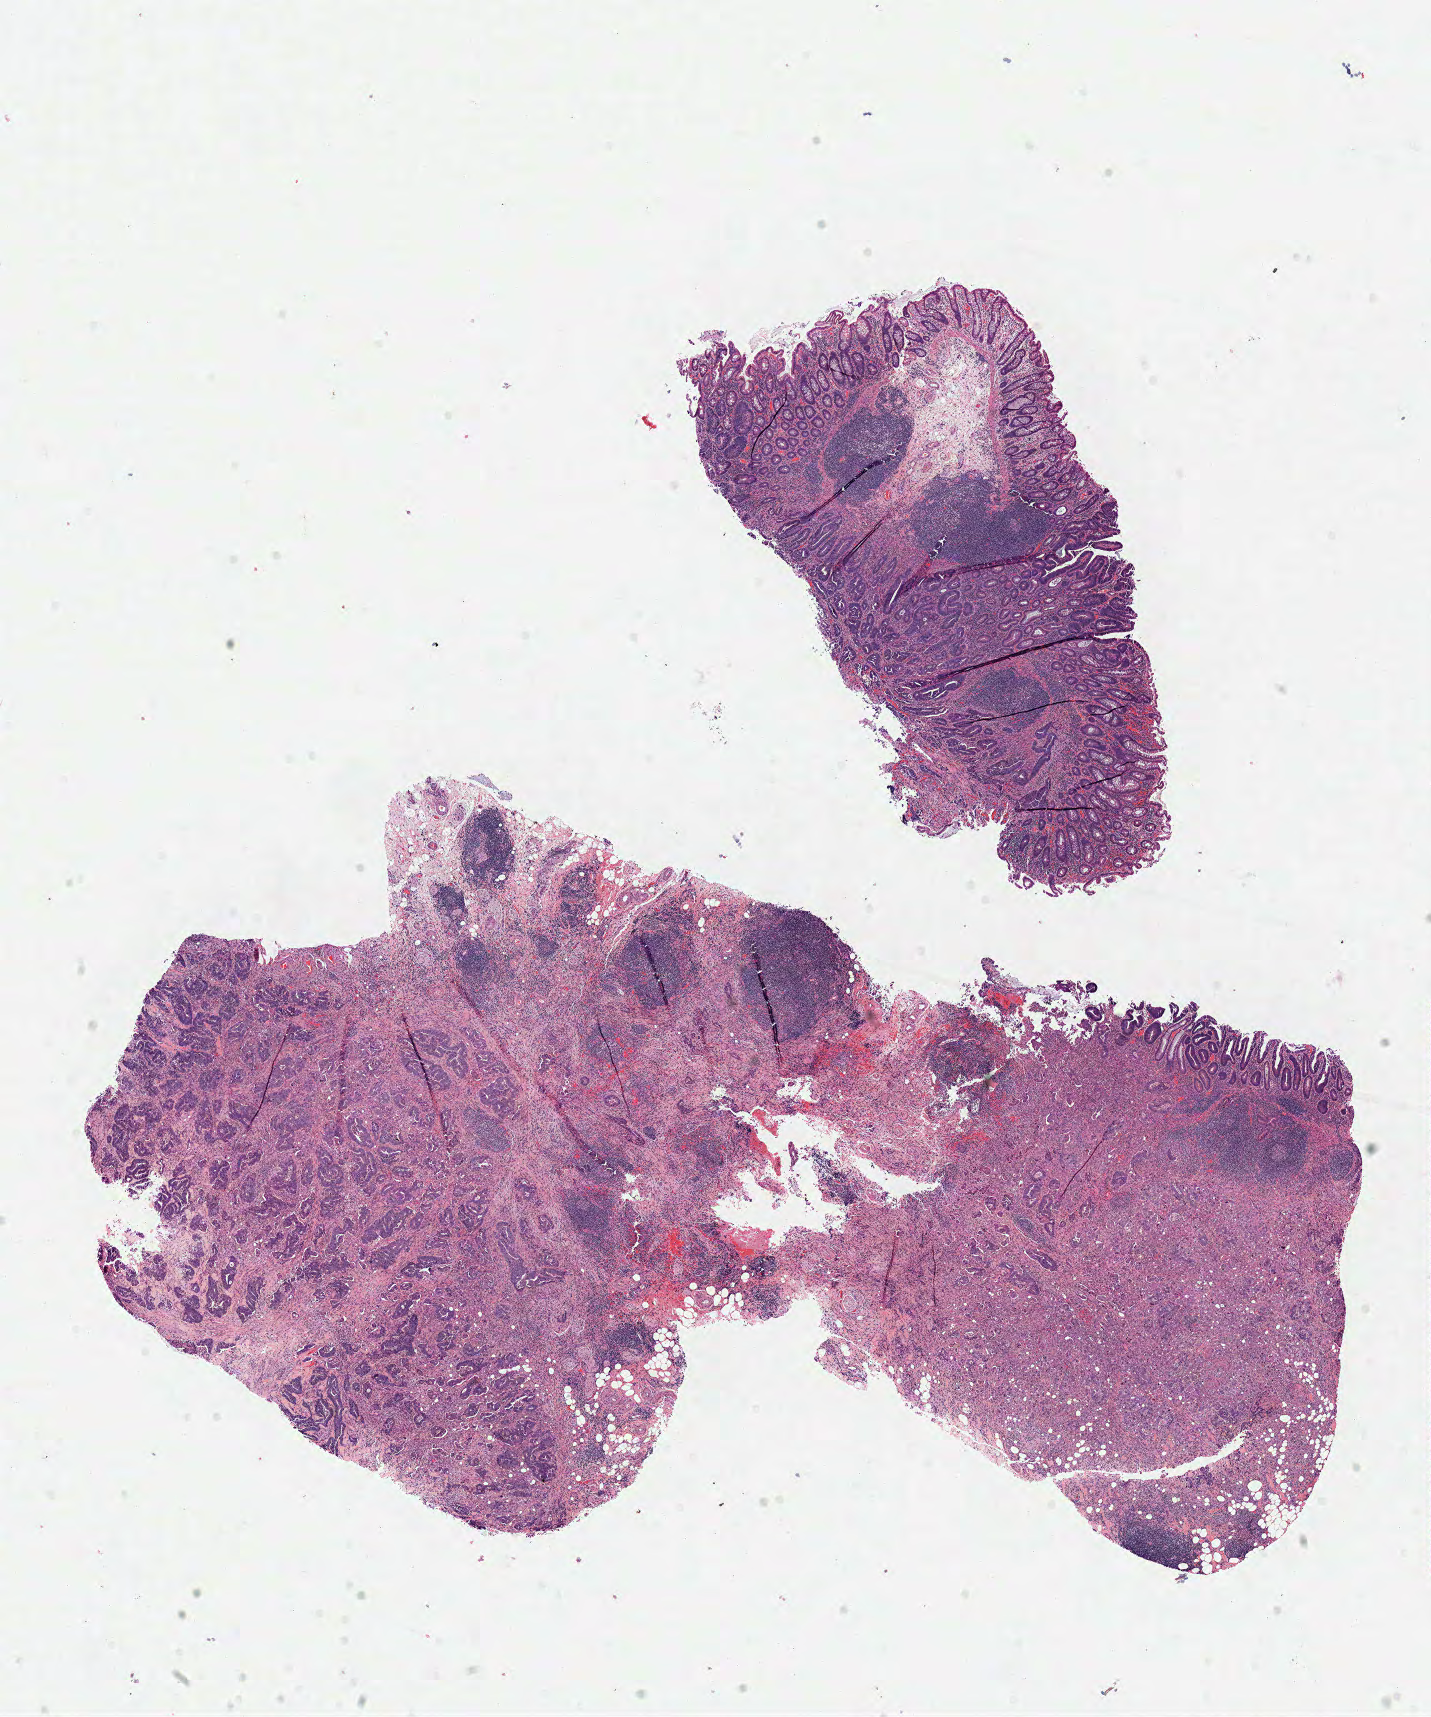
H&E whole-slide image — shown as a low-resolution overview of the whole scanned area (about 11.3 x 13.5 mm). Frozen section from the top of the tissue portion. Sample: primary tumour, colon. Male patient; age at initial diagnosis 80 years. Pathologist review of this section (percent, as recorded): tumour cells 60%, tumour nuclei 65%, normal cells 15%, stromal cells 20%, necrosis 5%.
• AJCC pathologic stage: III (6th edition)
• pathologic diagnosis: Adenocarcinoma, NOS (ascending colon)